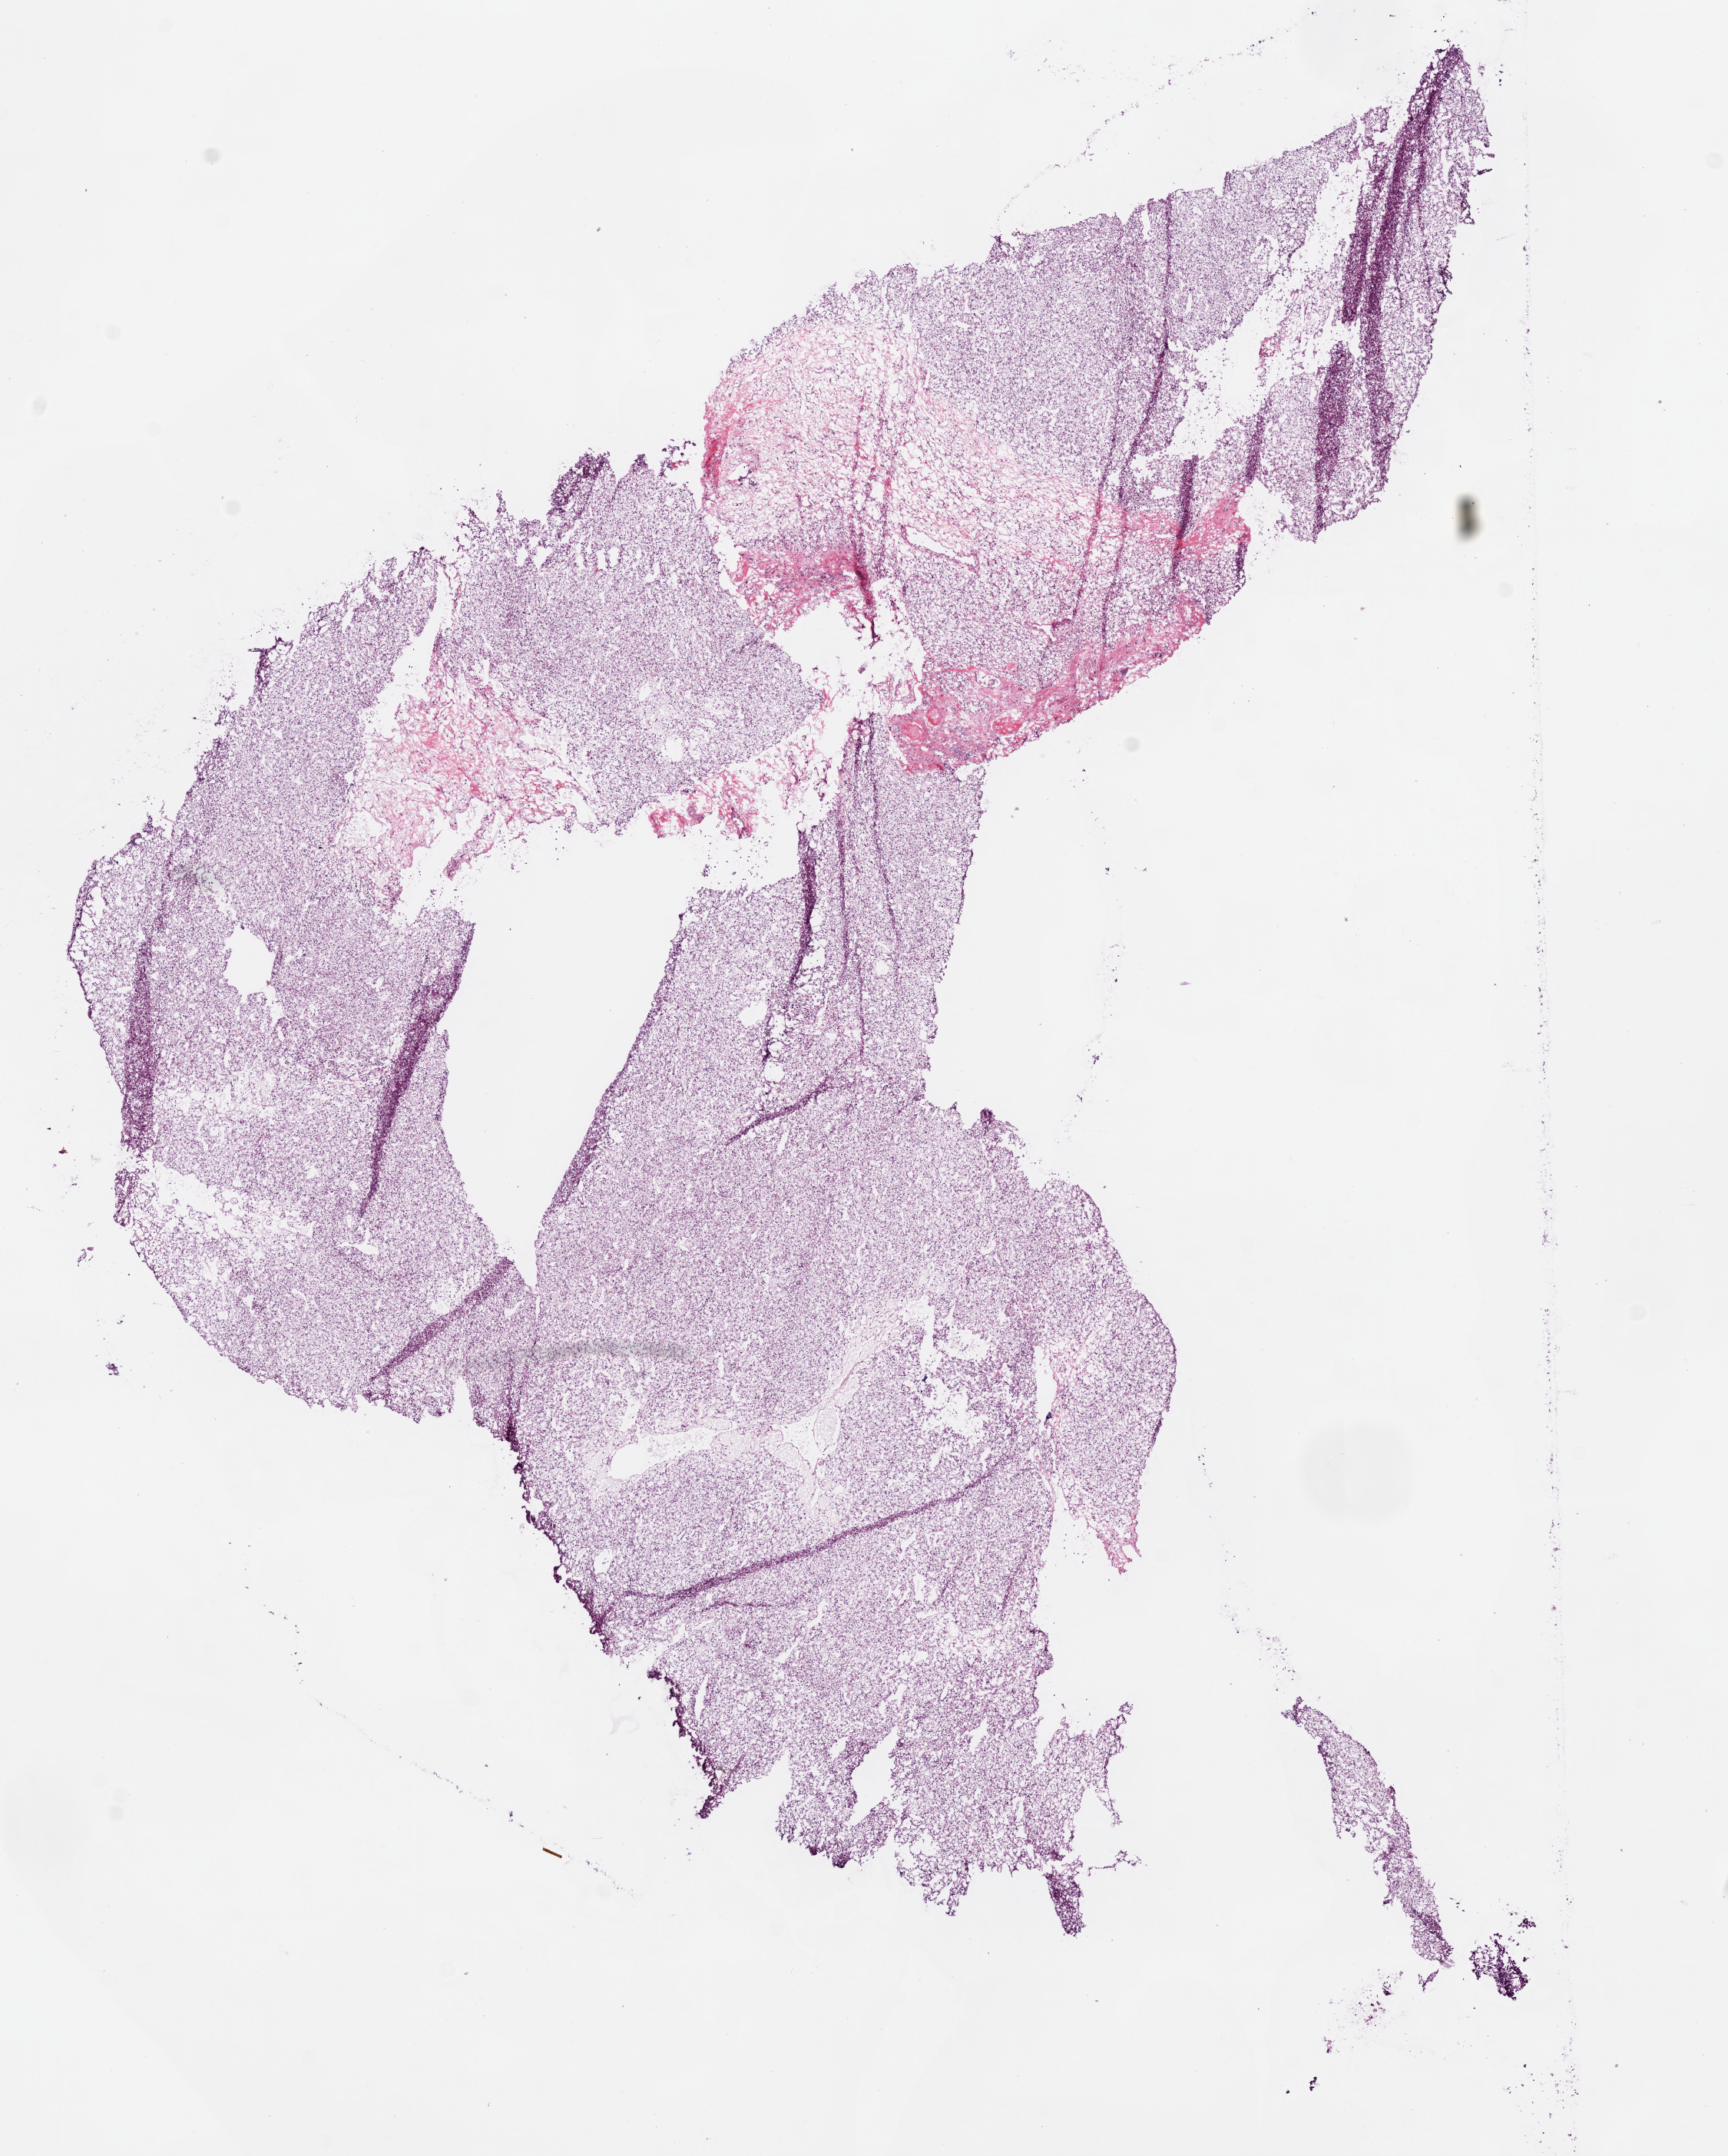
H&E-stained whole-slide image, shown as a low-resolution overview of the whole scanned area (about 9.0 x 11.3 mm, from a 20x scan). Frozen section from the bottom of the tissue portion. Sample: primary tumour, kidney. Female, age 73 years at initial diagnosis. Histologic grade: G2 (moderately differentiated). Composition of this section per pathologist review: tumour cells 85%, tumour nuclei 90%, normal cells 0%, stromal cells 15%, necrosis 0%.
AJCC pathologic stage: I (7th edition). Laterality: left. Pathologic diagnosis: Clear cell adenocarcinoma, NOS. TNM: T1a N0 M0.